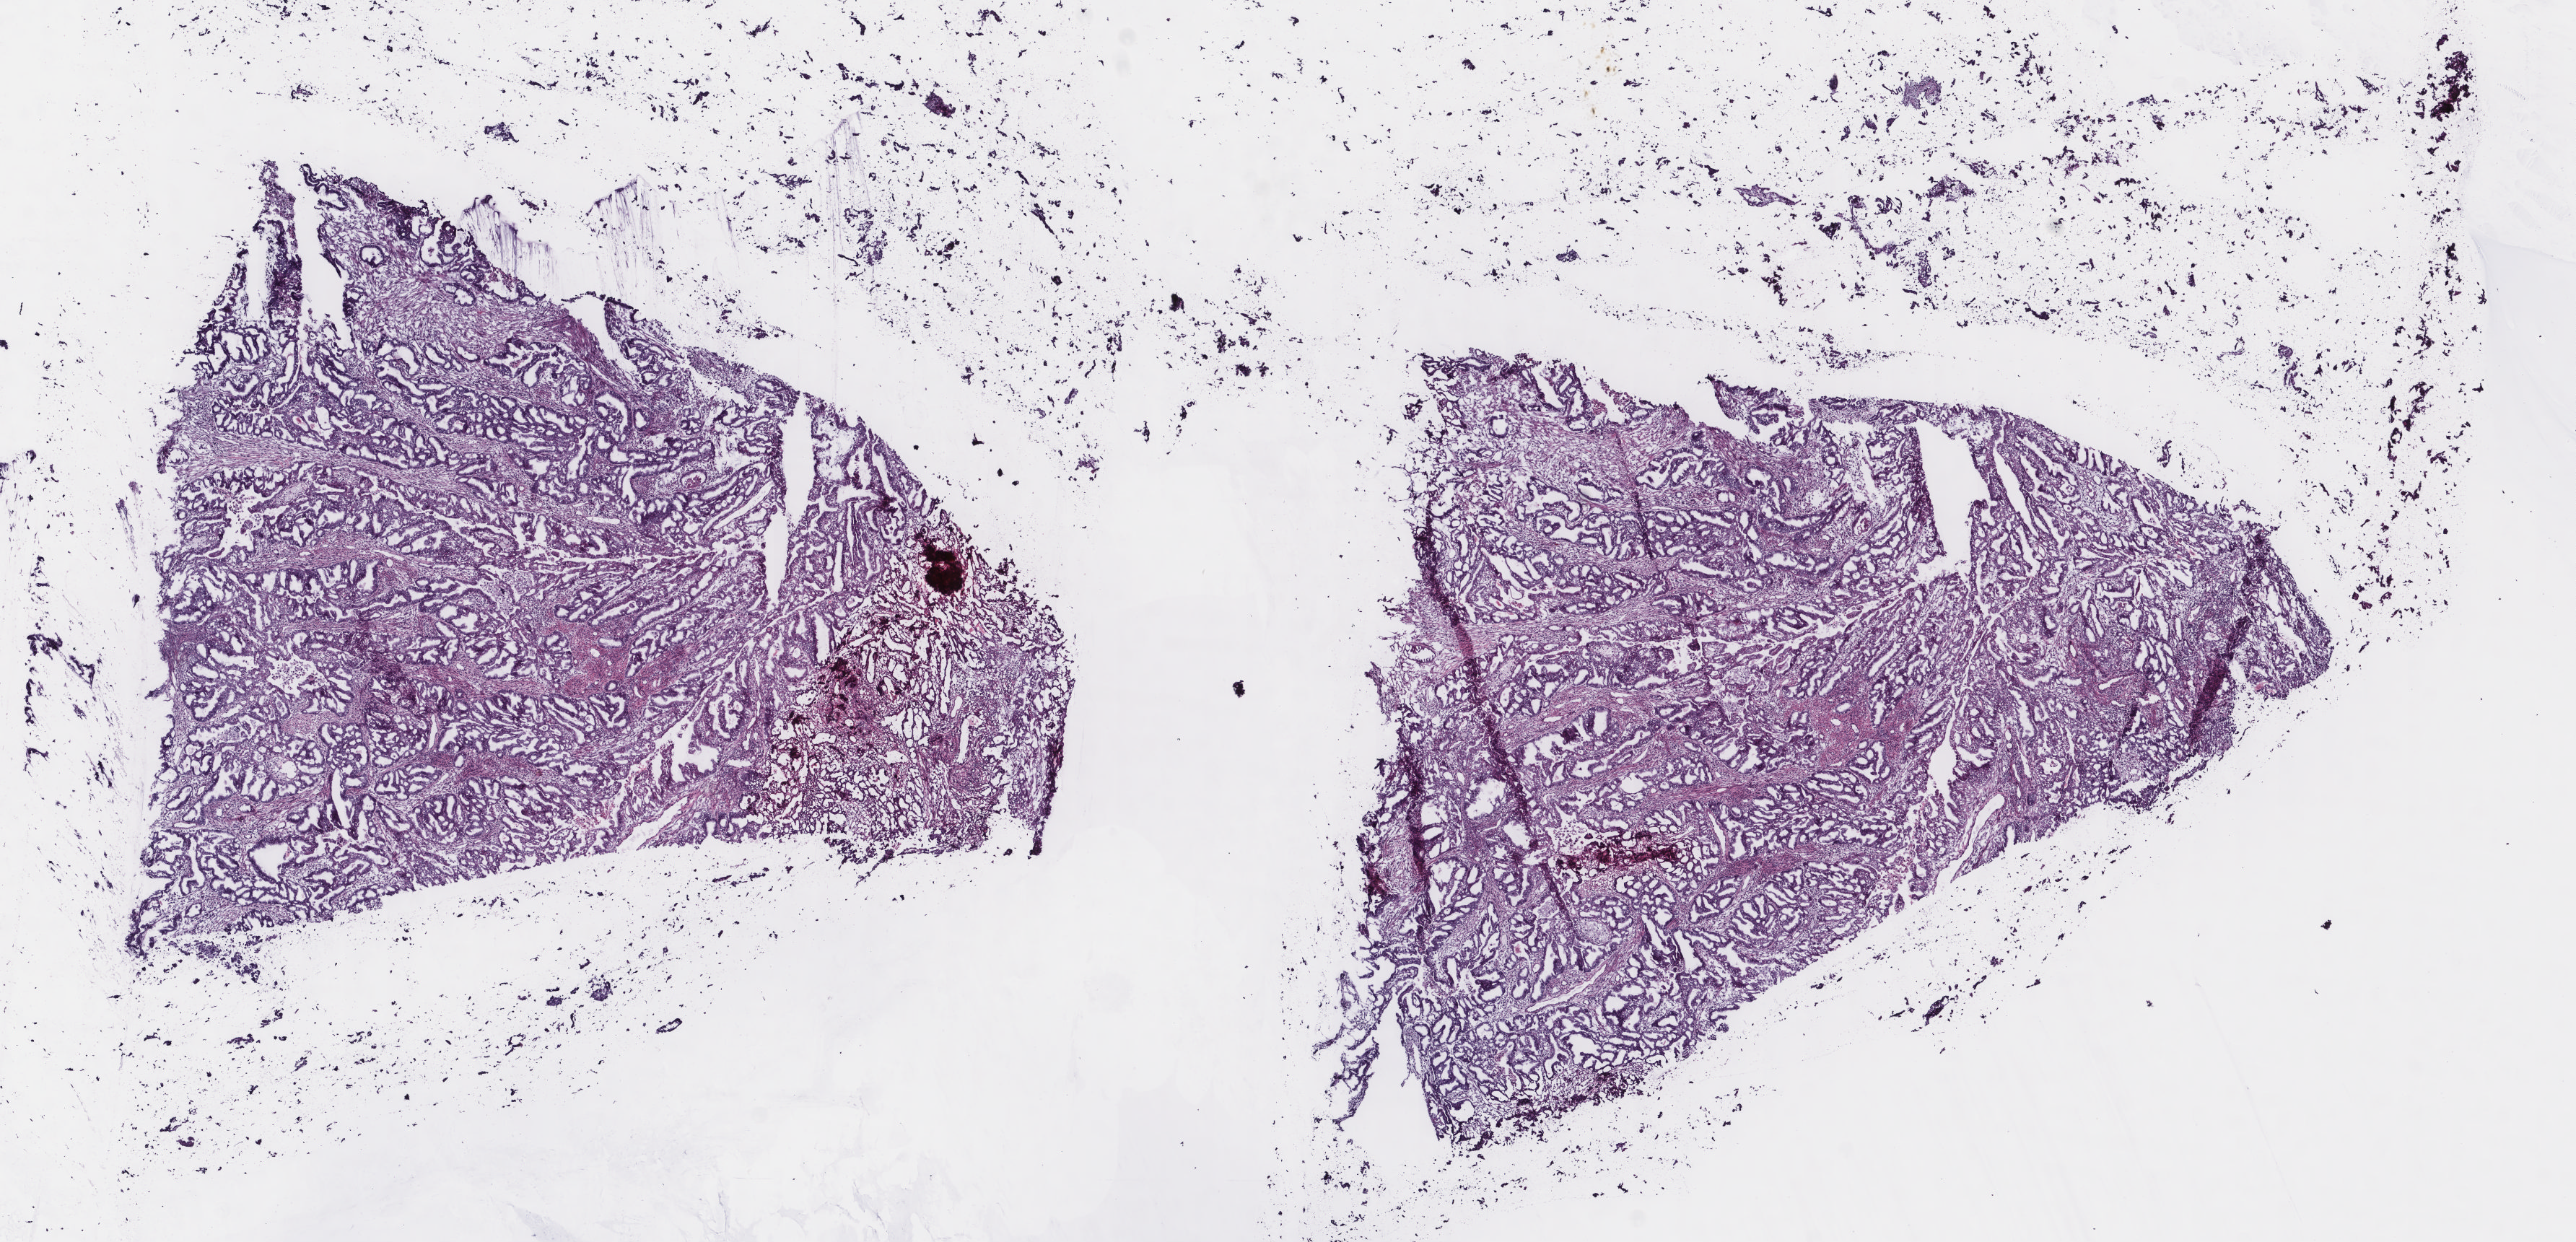
Digitized H&E tissue section (whole slide) — low-resolution overview of the scanned area, about 14.2 x 6.8 mm; frozen section; primary tumour sample from the uterus. Female, age 53 years at initial diagnosis. Histologic grade: G2 (moderately differentiated). Slide review estimates, as recorded: tumour cells 100%, tumour nuclei 65%, normal cells 0%, stromal cells 0%, necrosis 0%. Inflammatory infiltration, as recorded: lymphocyte infiltration 0%, monocyte infiltration 0%, neutrophil infiltration 0%.
- FIGO stage: IIIC2
- lymph nodes positive (case pathology): 0 of 3 examined
- histologic diagnosis: Endometrioid adenocarcinoma, NOS